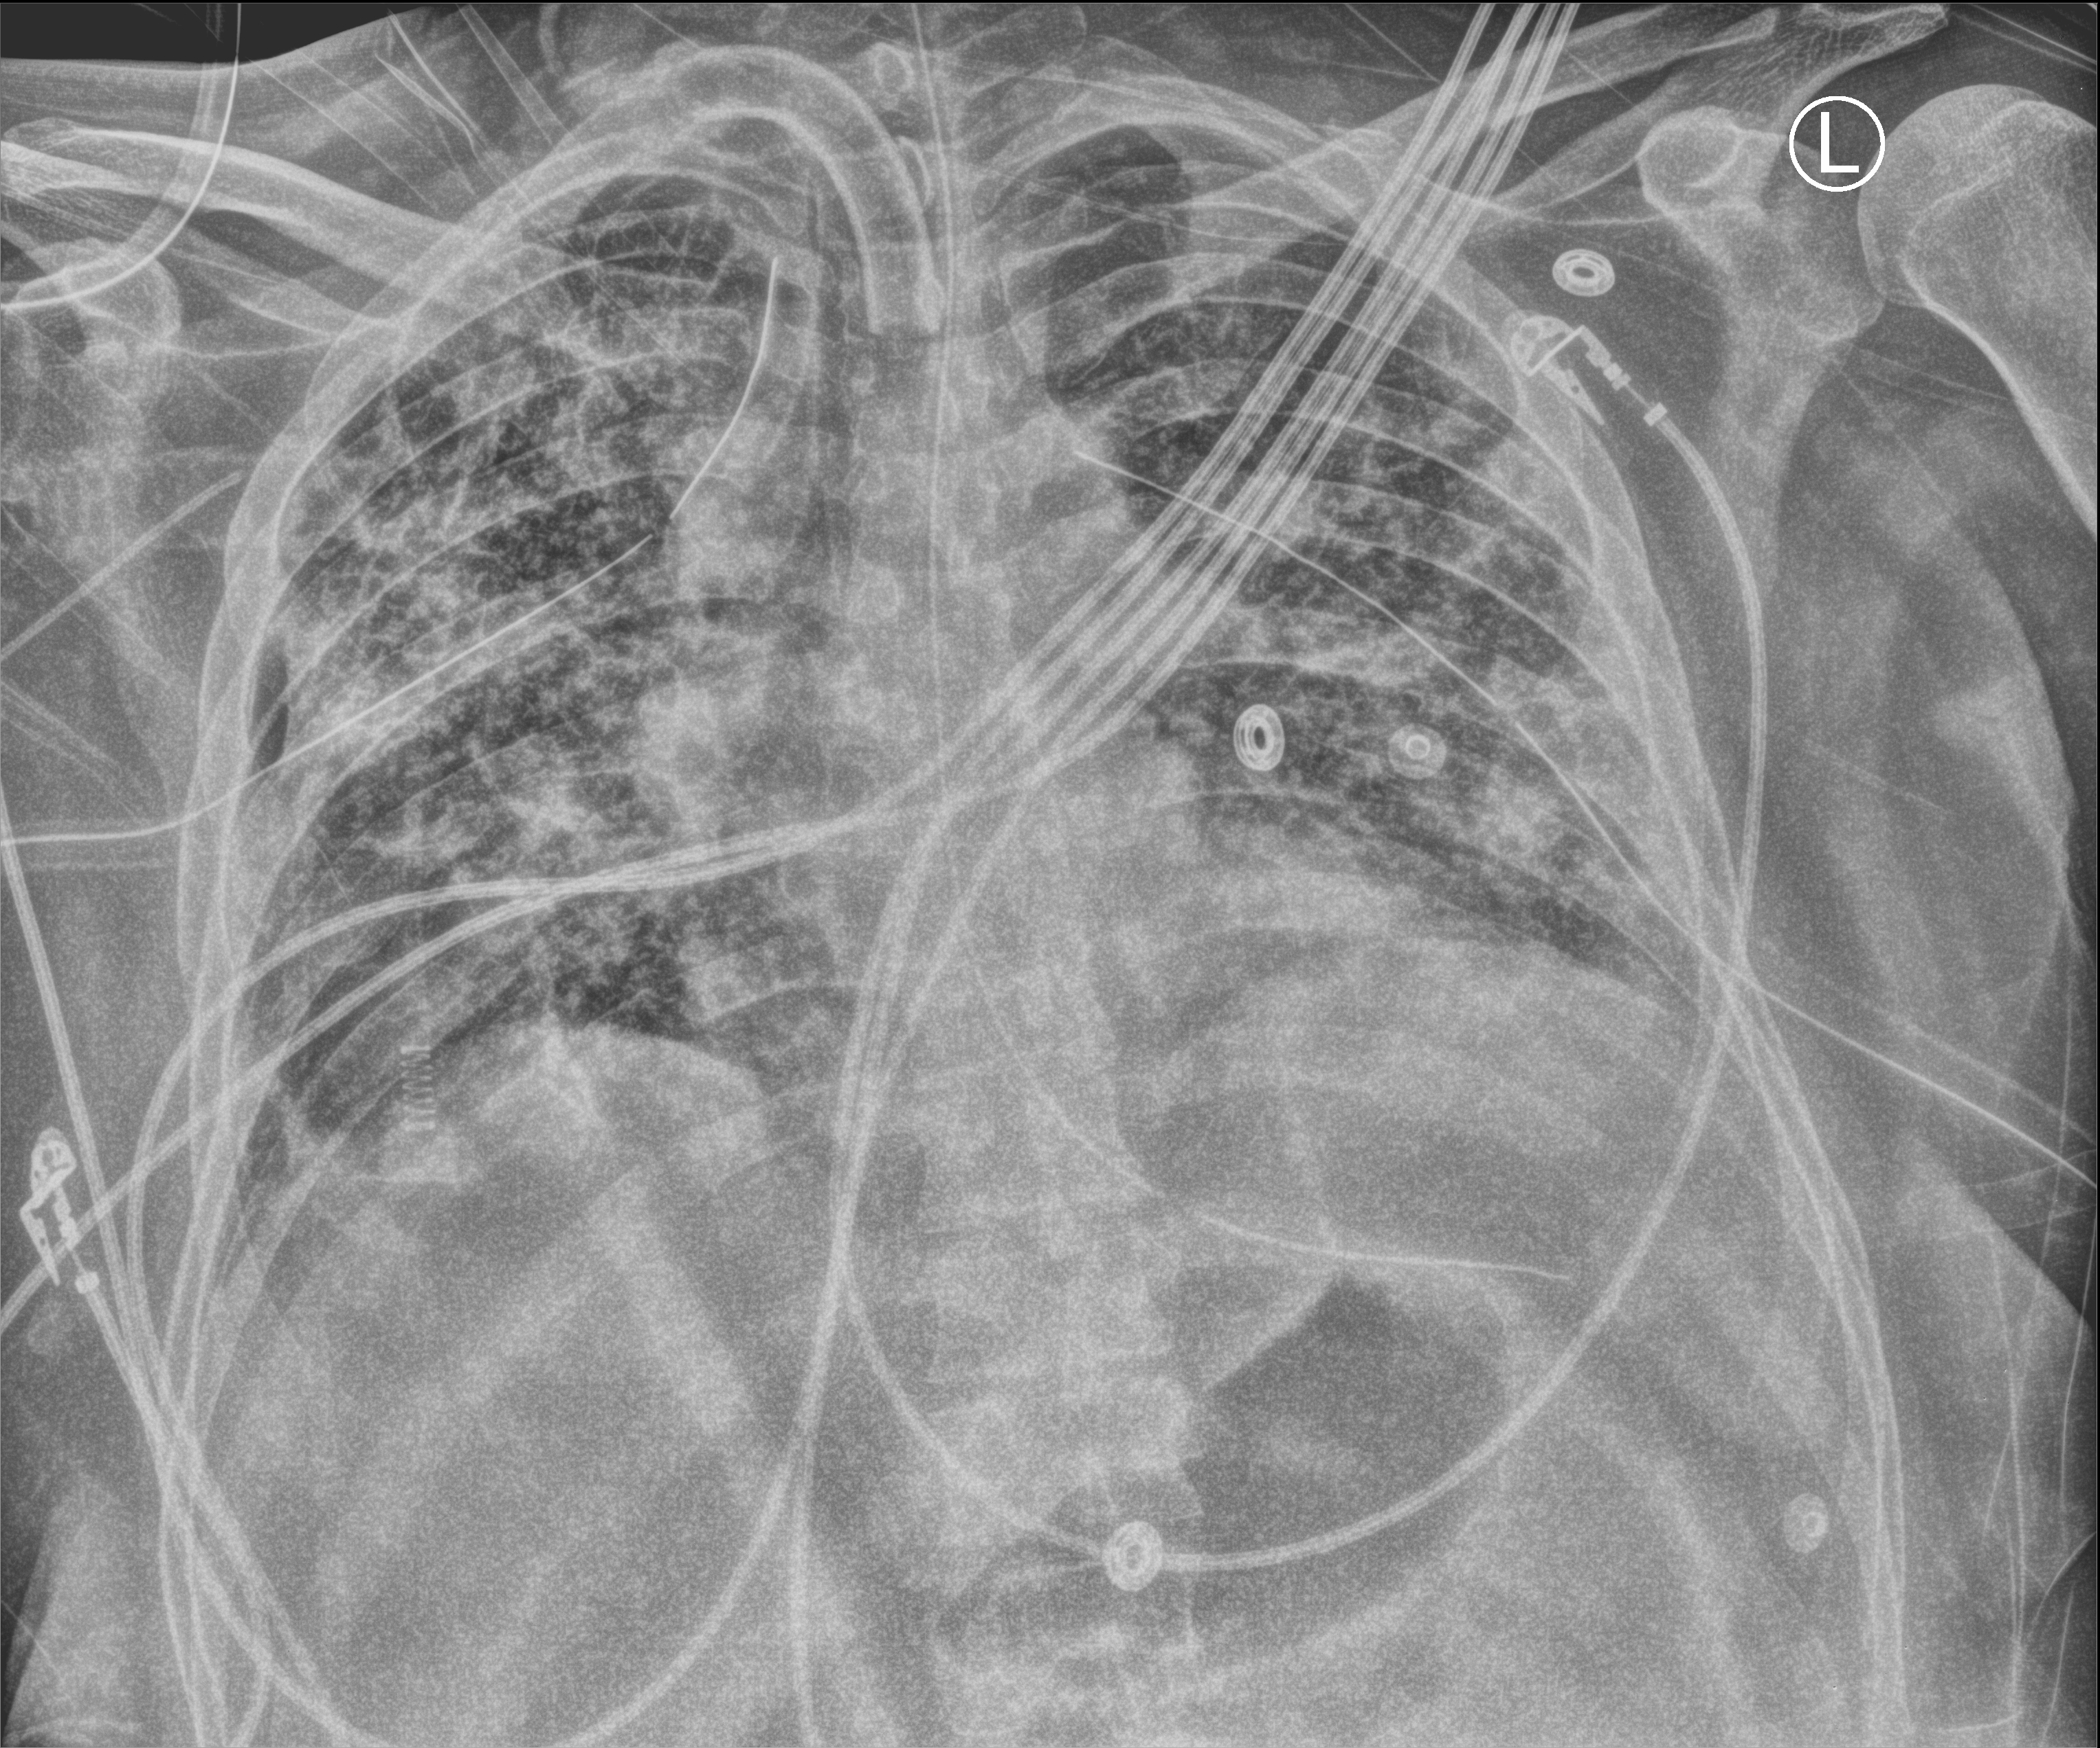
Portable chest radiograph, anteroposterior (AP) projection. Patient hospitalised with COVID-19; male, aged 18–59 years.
Hospital-stay facts (about this admission, not read from this image; timing relative to this image not recorded):
- admitted to intensive care during this hospital stay: yes
- mechanically ventilated during this hospital stay: yes